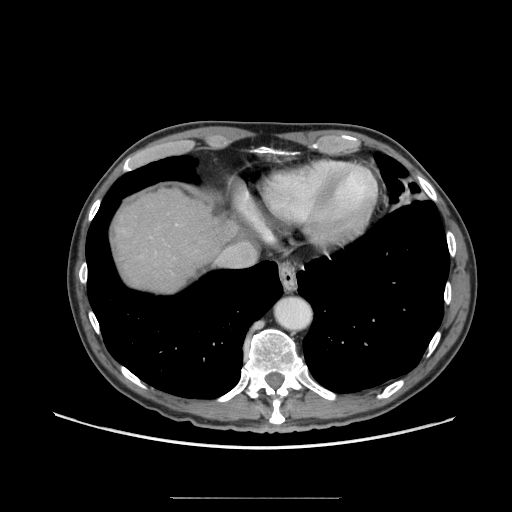
Contrast-enhanced abdominal CT (liver protocol), one axial slice. Slice 61 of 71 in the series (ordered by position). Soft-tissue window (W 400 / L 40 HU). 2.5 mm slice thickness. 512 × 512 image matrix. Case-level facts recorded for this patient, not image findings: diagnosis: hepatocellular carcinoma (patient treated with transarterial chemoembolisation; whether this scan precedes or follows treatment is not stated here); TNM stage (as recorded): Stage-I; Child-Pugh class: A; tumour differentiation: well differentiated; tumour nodularity: uninodular.
Annotated regions visible in this slice (semi-automatic segmentation, software-assisted and operator-edited):
- abdominal aorta: box from (x=275, y=297) to (x=310, y=330) px
- liver parenchyma outside the tumour (the mass and vessels are separate outlines, so this box may not span the whole liver): (x=114, y=190)–(x=244, y=292)
- mass: (x=112, y=217)–(x=127, y=234)